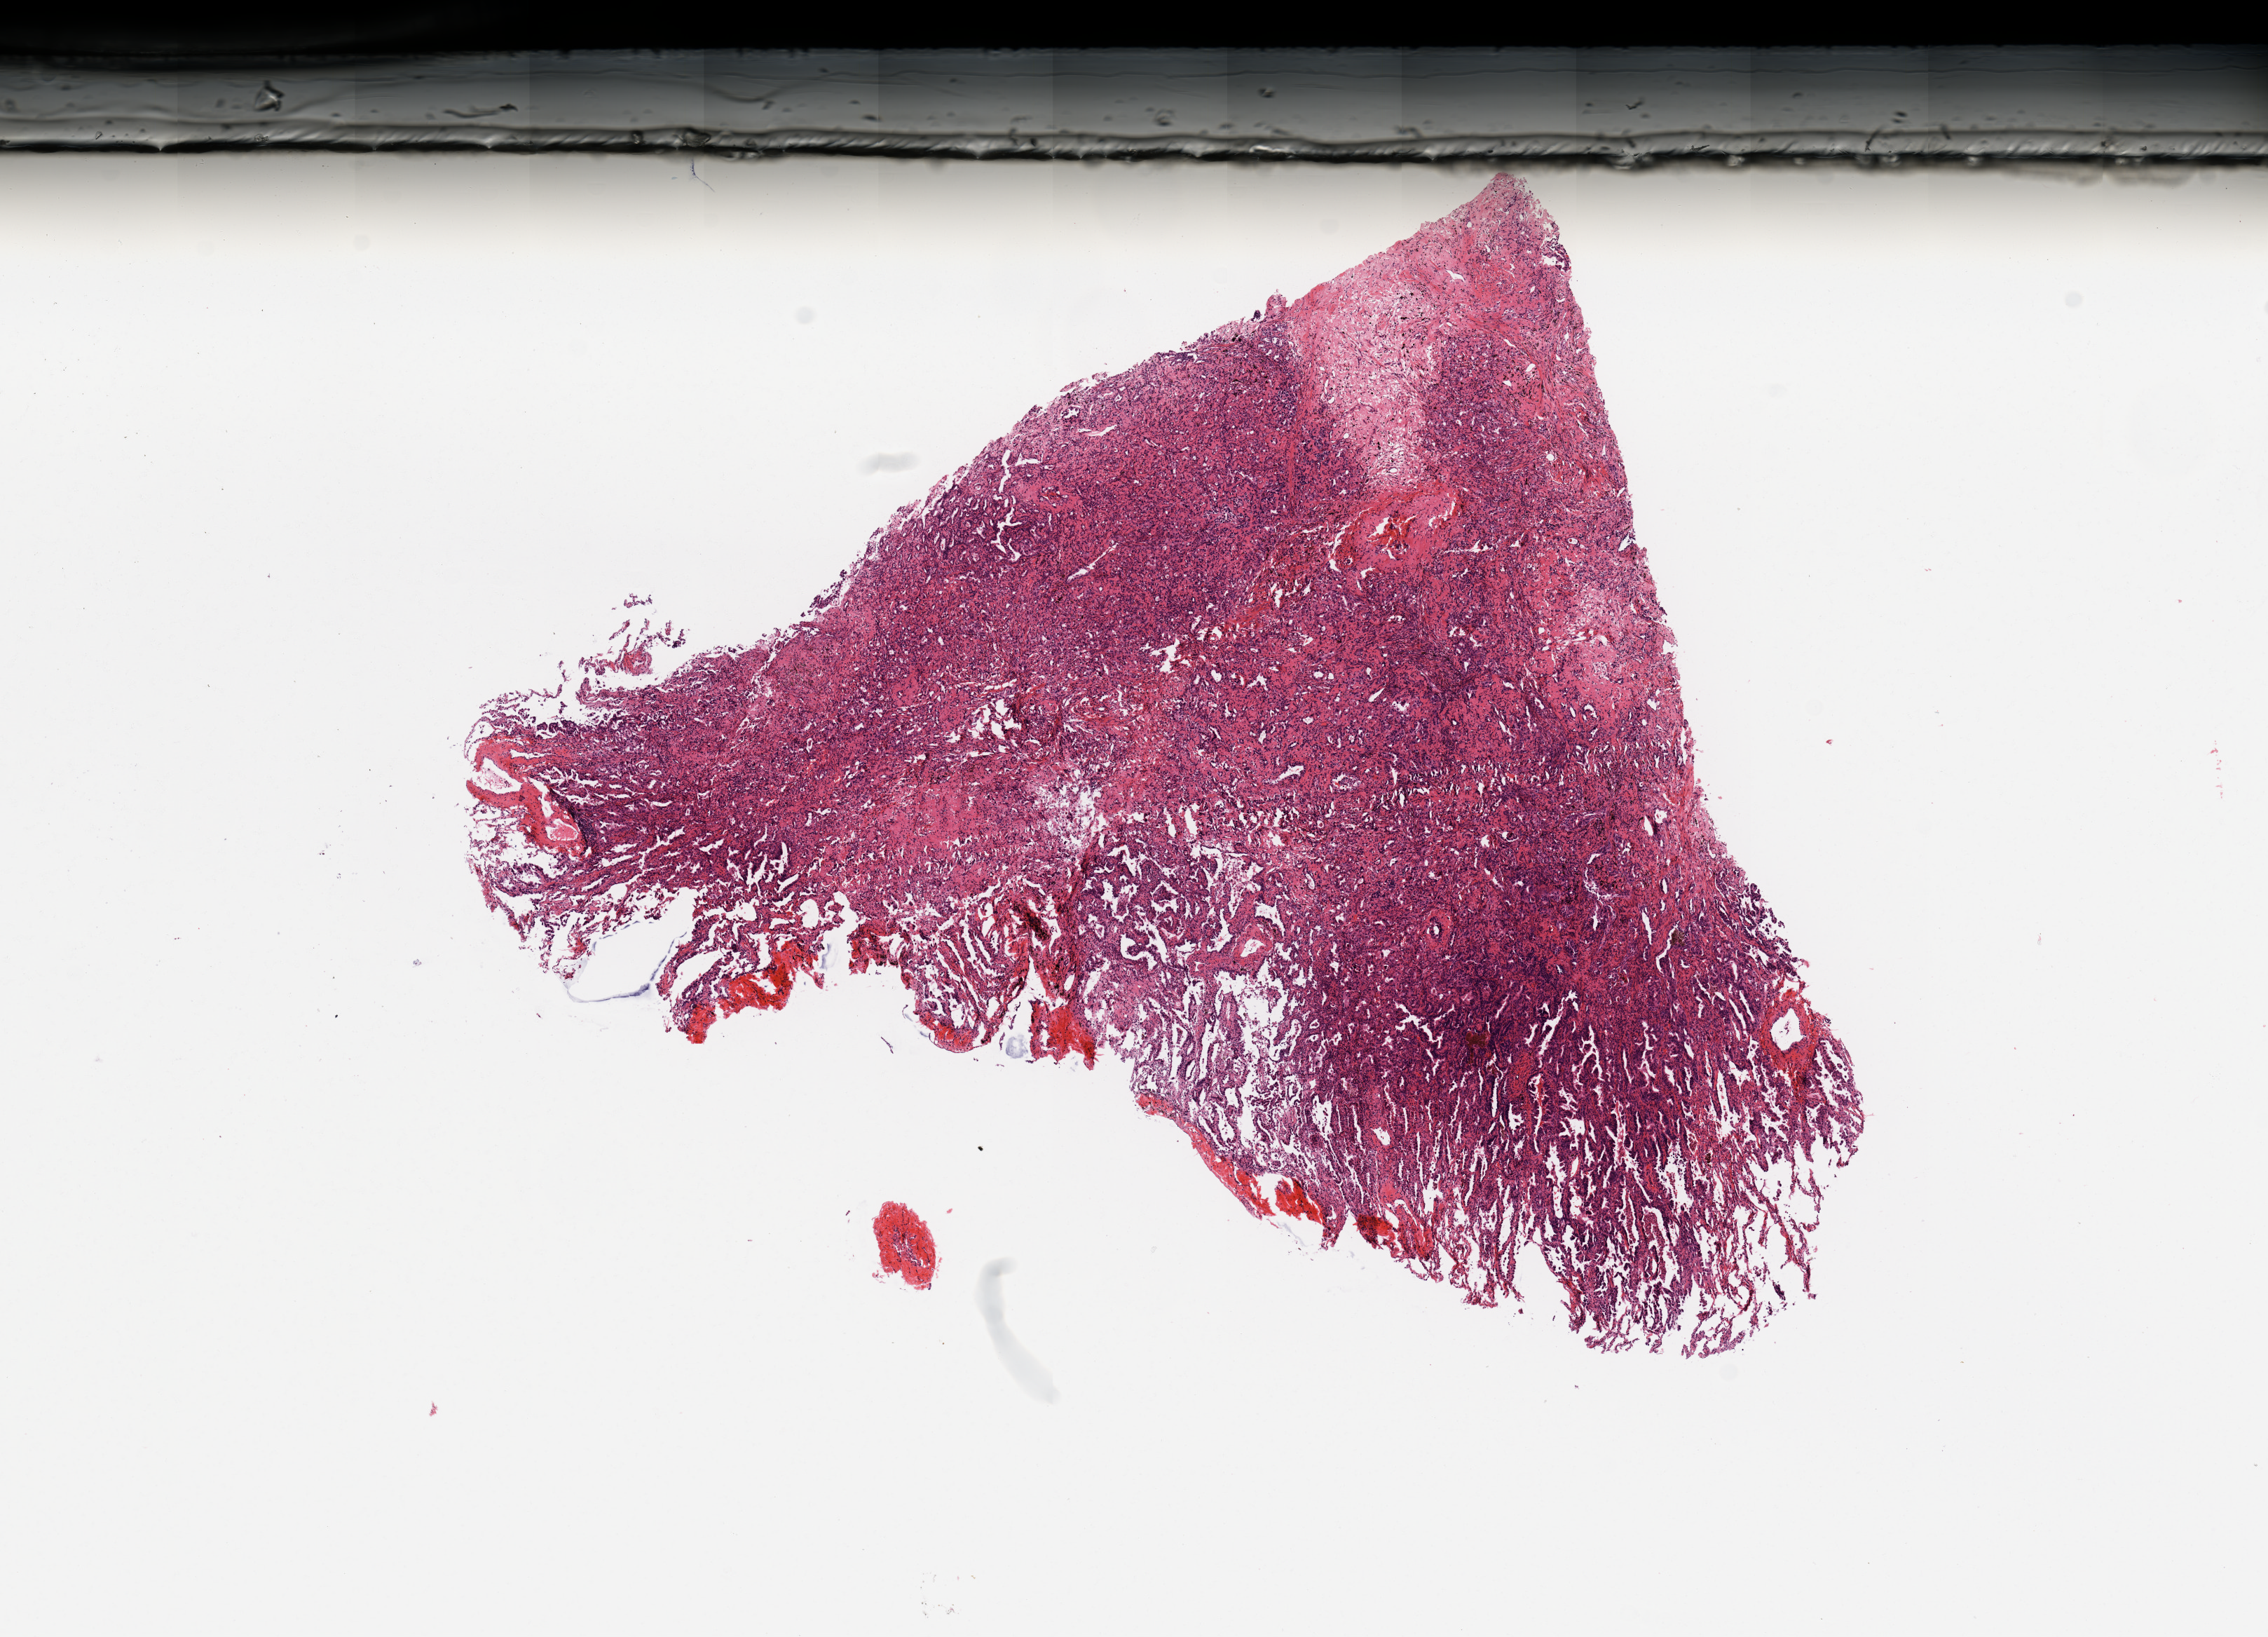
Digitized H&E tissue section (whole slide), whole scanned area (about 12.8 x 9.2 mm, acquisition: 20x scan) shown as a low-resolution overview; tumour tissue sample, sampled site: lung. Female, 37 y/o. Histologic grade: G2 (moderately differentiated). Pathologist review of this section (percent, as recorded): tumour nuclei 80%, necrosis 2%.
* primary tumour site (as recorded): left upper lobe
* AJCC pathologic stage: IIIA
* diagnosis: Adenocarcinoma, NOS